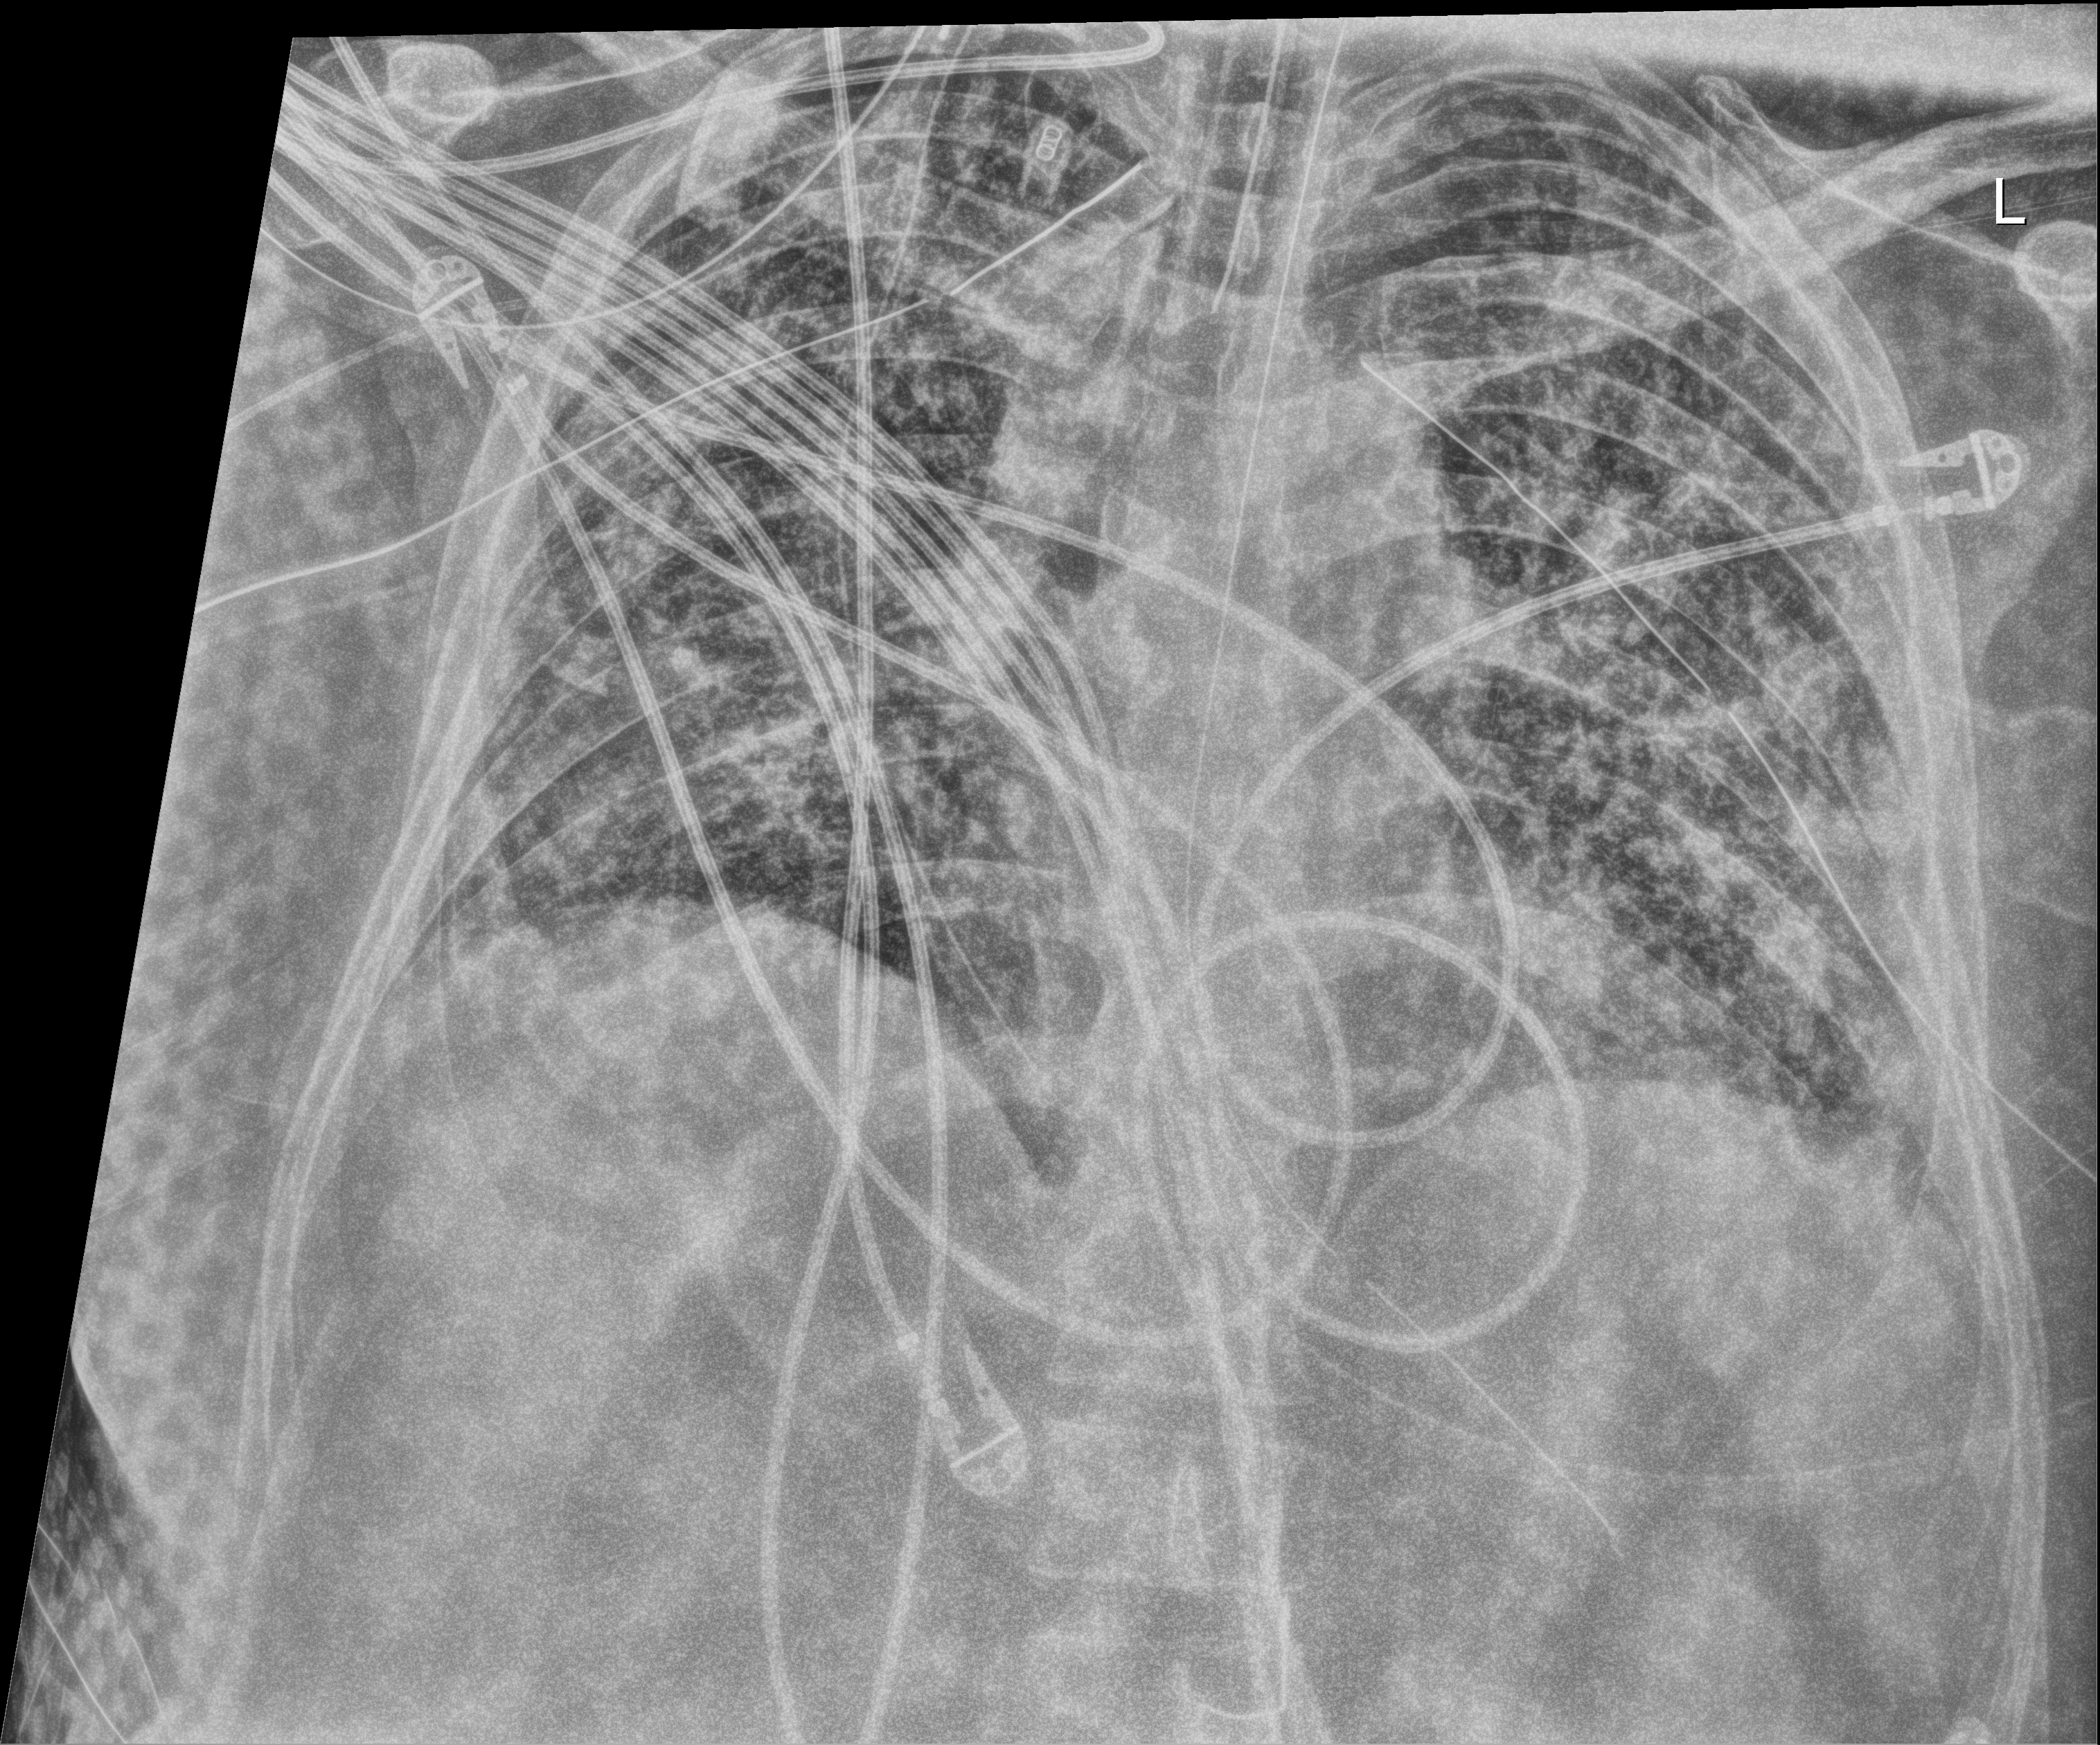
Chest X-ray (portable). Patient hospitalised with COVID-19; male, aged 18–59 years.
From the hospital-stay record, not from the radiograph (when in the stay this image was taken is not recorded):
- smoking status (admission record): never
- admitted to intensive care during this hospital stay: yes